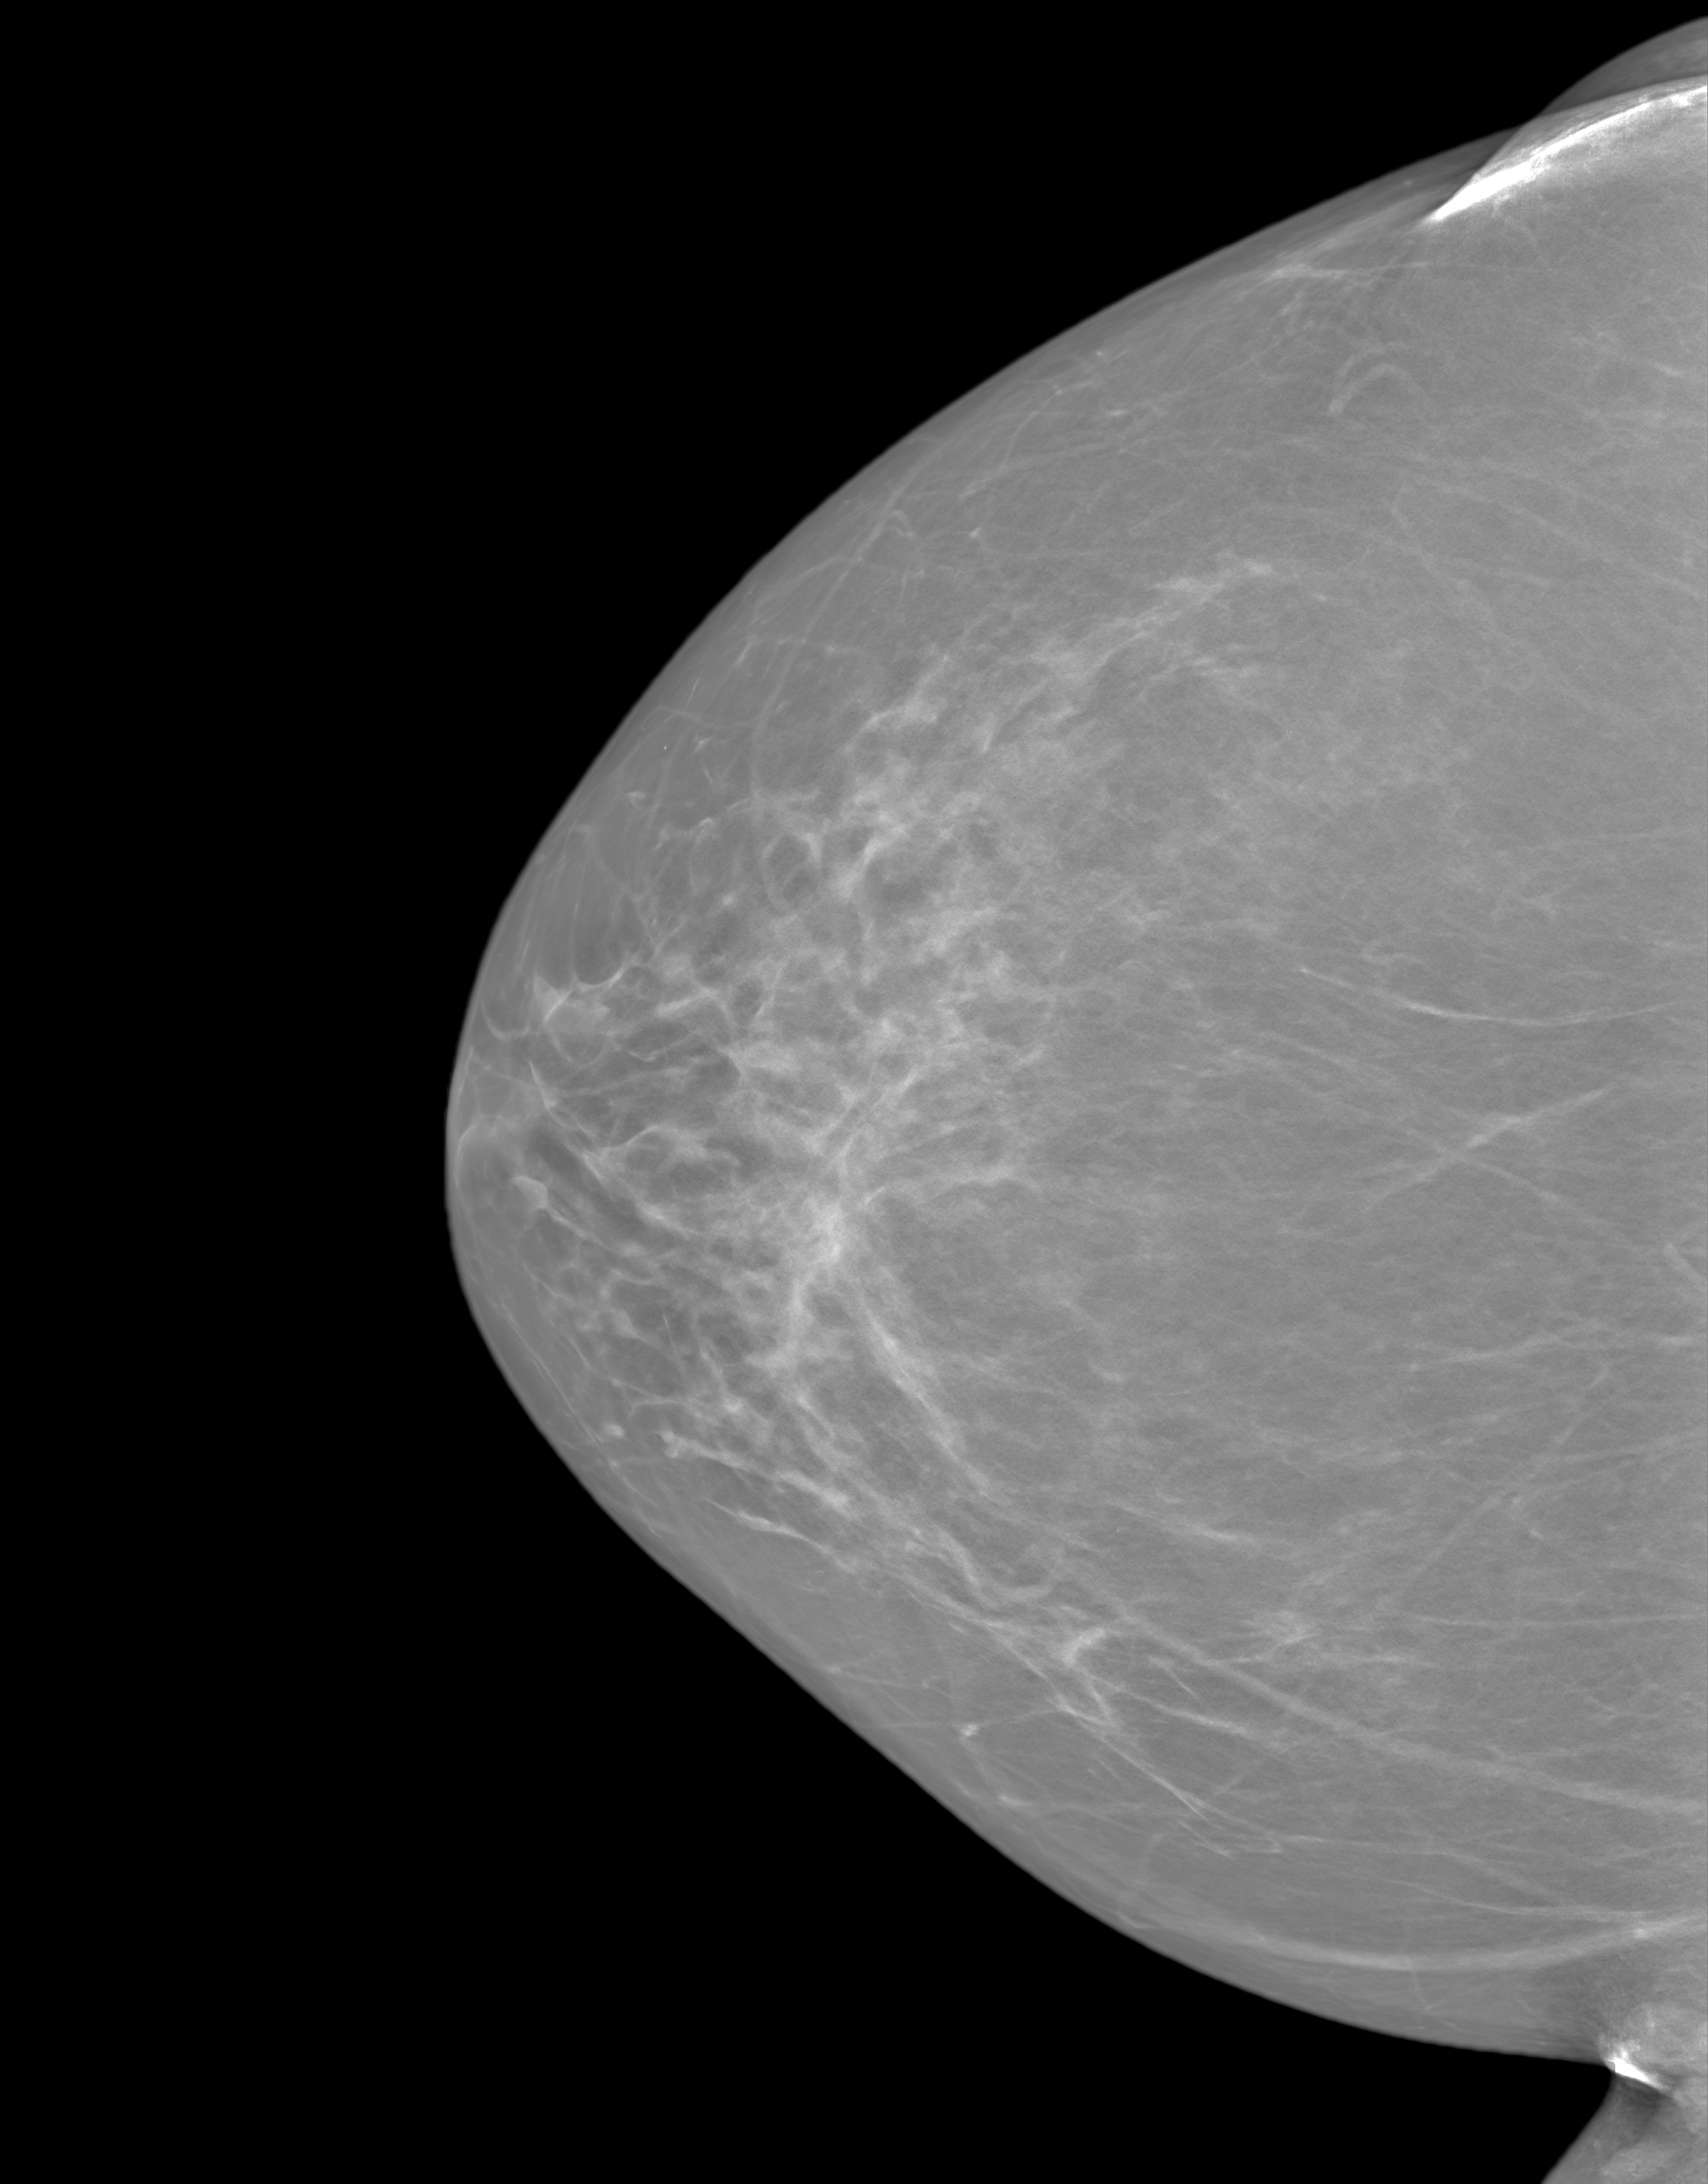
Screening examination, system: SenoIris_1SP1.1(421). Patient: female, 58 years.
Image type: synthesized 2-D view from tomosynthesis. Breast: right. Projection: craniocaudal (CC) view.